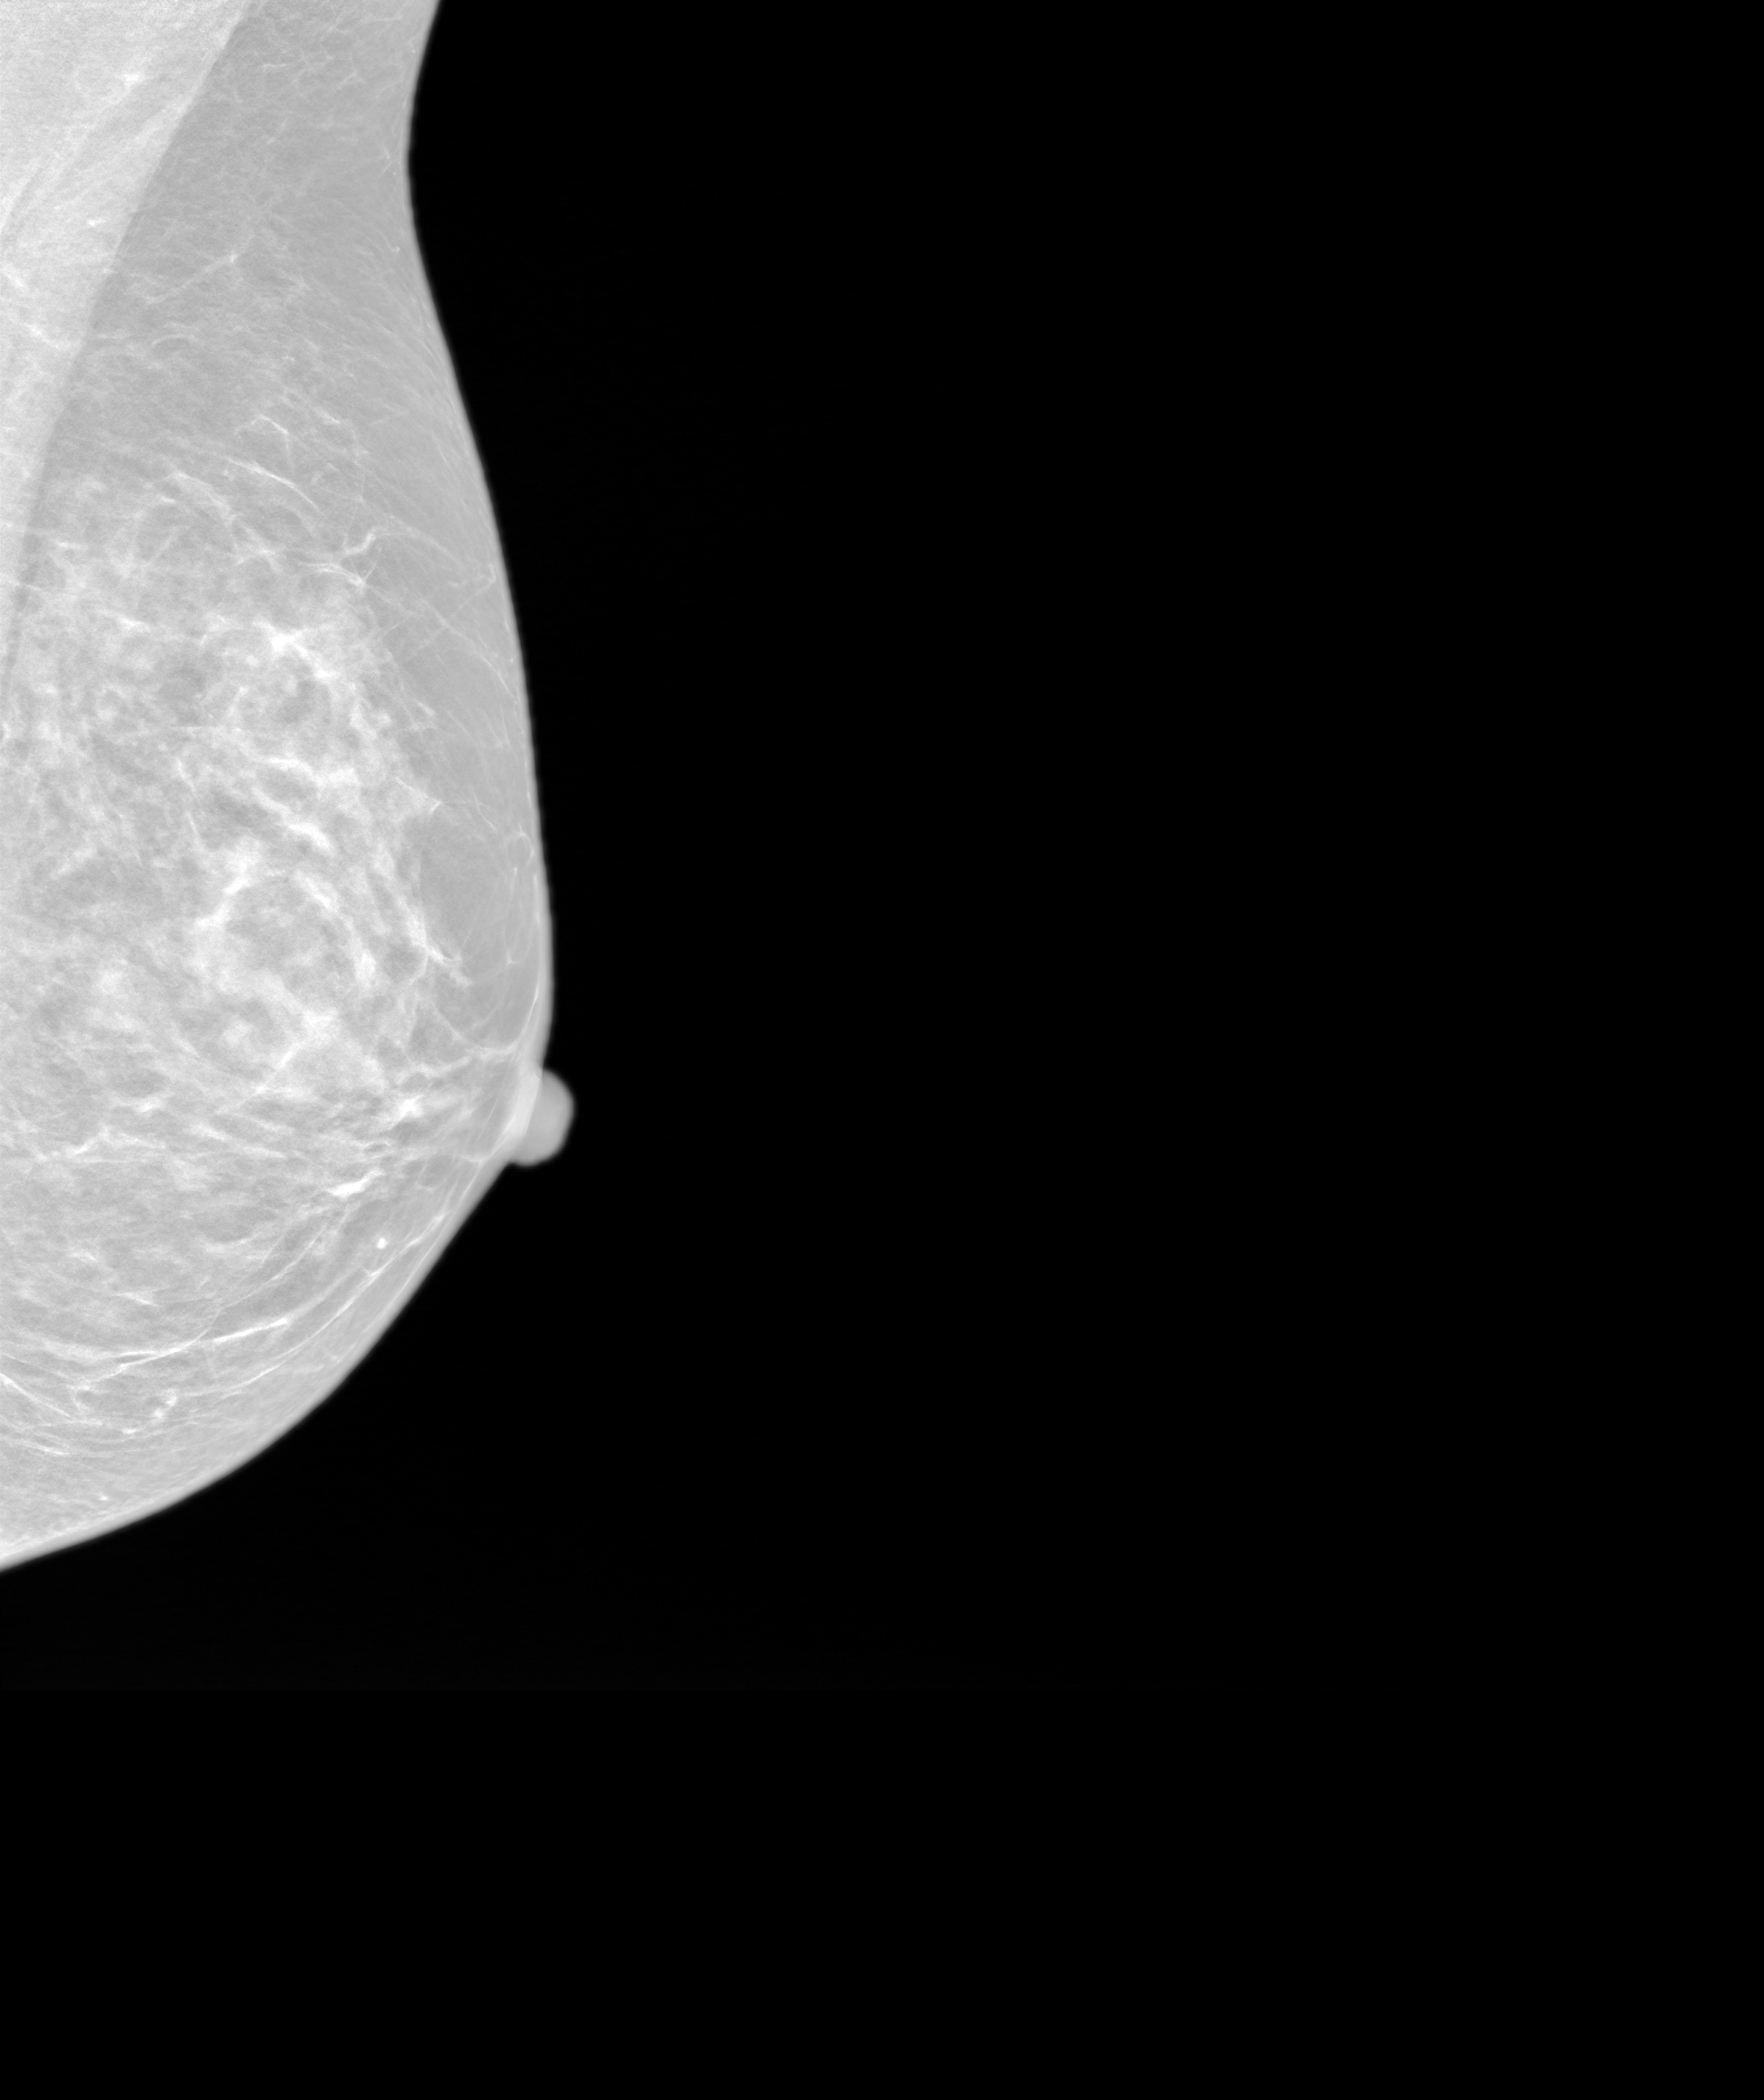
Annual screening mammography examination, system: SenoIris_1SP2(440). Patient aged 62 years (female).
Image type: synthesized 2-D view from tomosynthesis. Breast: left. Projection: medio-lateral oblique projection.